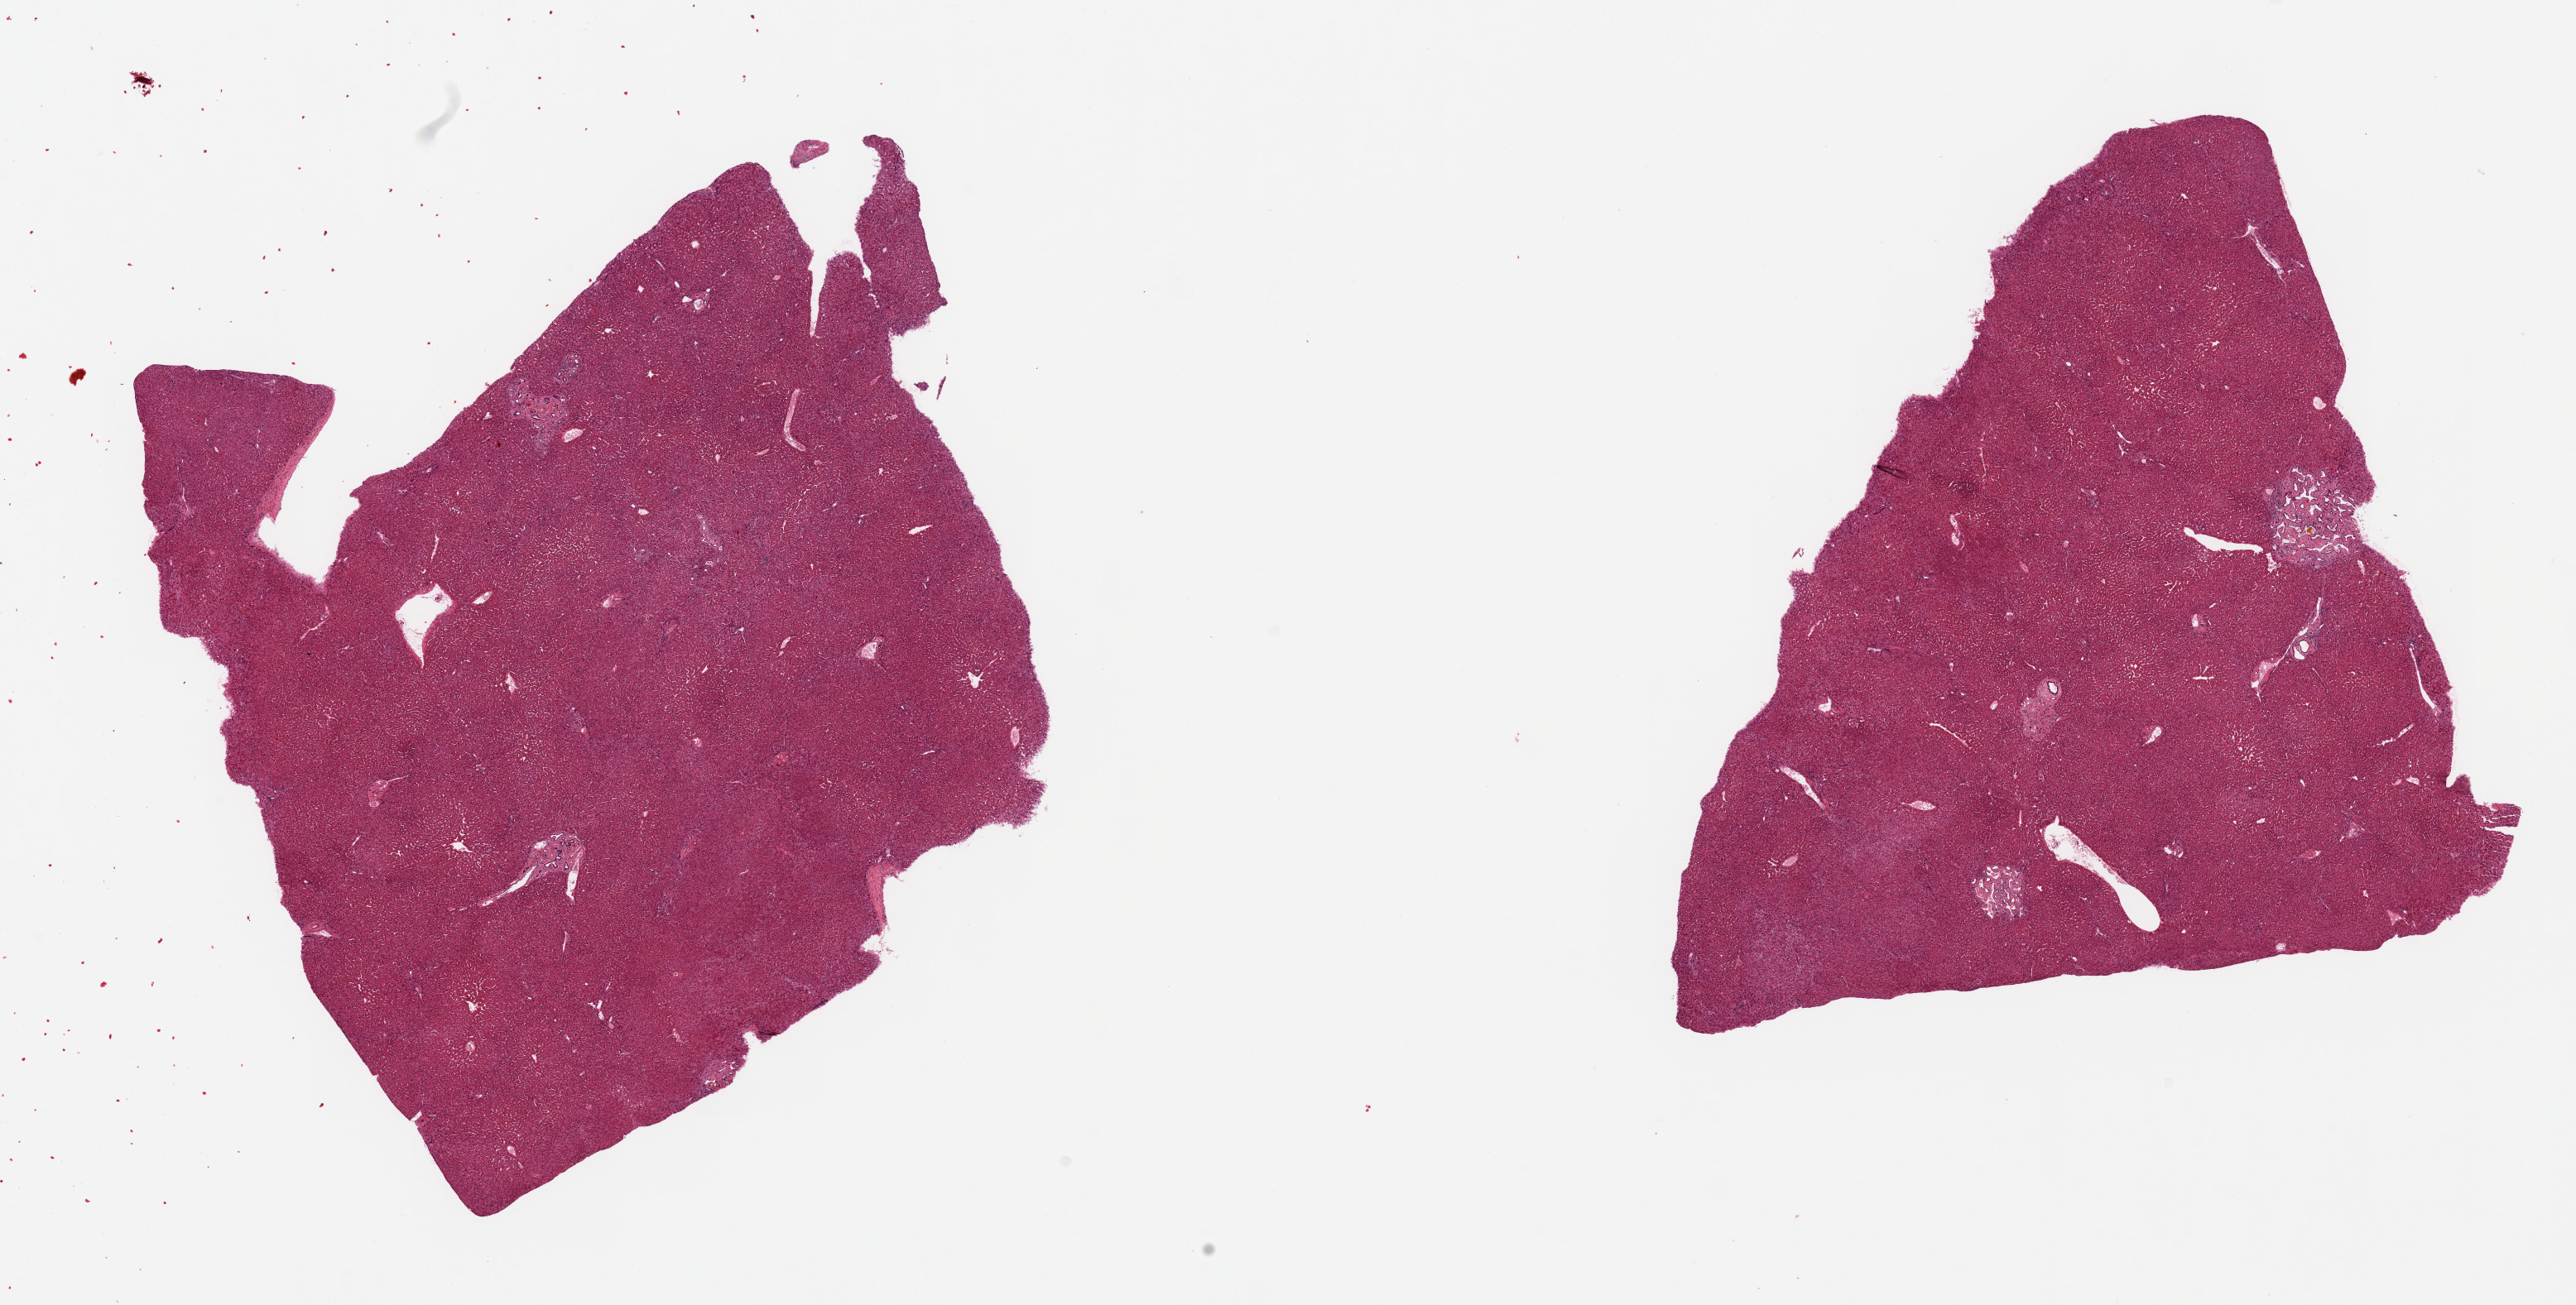
Hematoxylin and eosin (H&E) whole-slide image — whole scanned area (about 24.6 x 12.5 mm) shown as a low-resolution overview, PAXgene-fixed paraffin-embedded (PFPE) section, section of liver (target tissue), tissue donor sample. Female donor.
- review note (as recorded): 2 pieces, minimal steatosis, mulitple bile duct hamartomata (Meyenberg Complex) noted